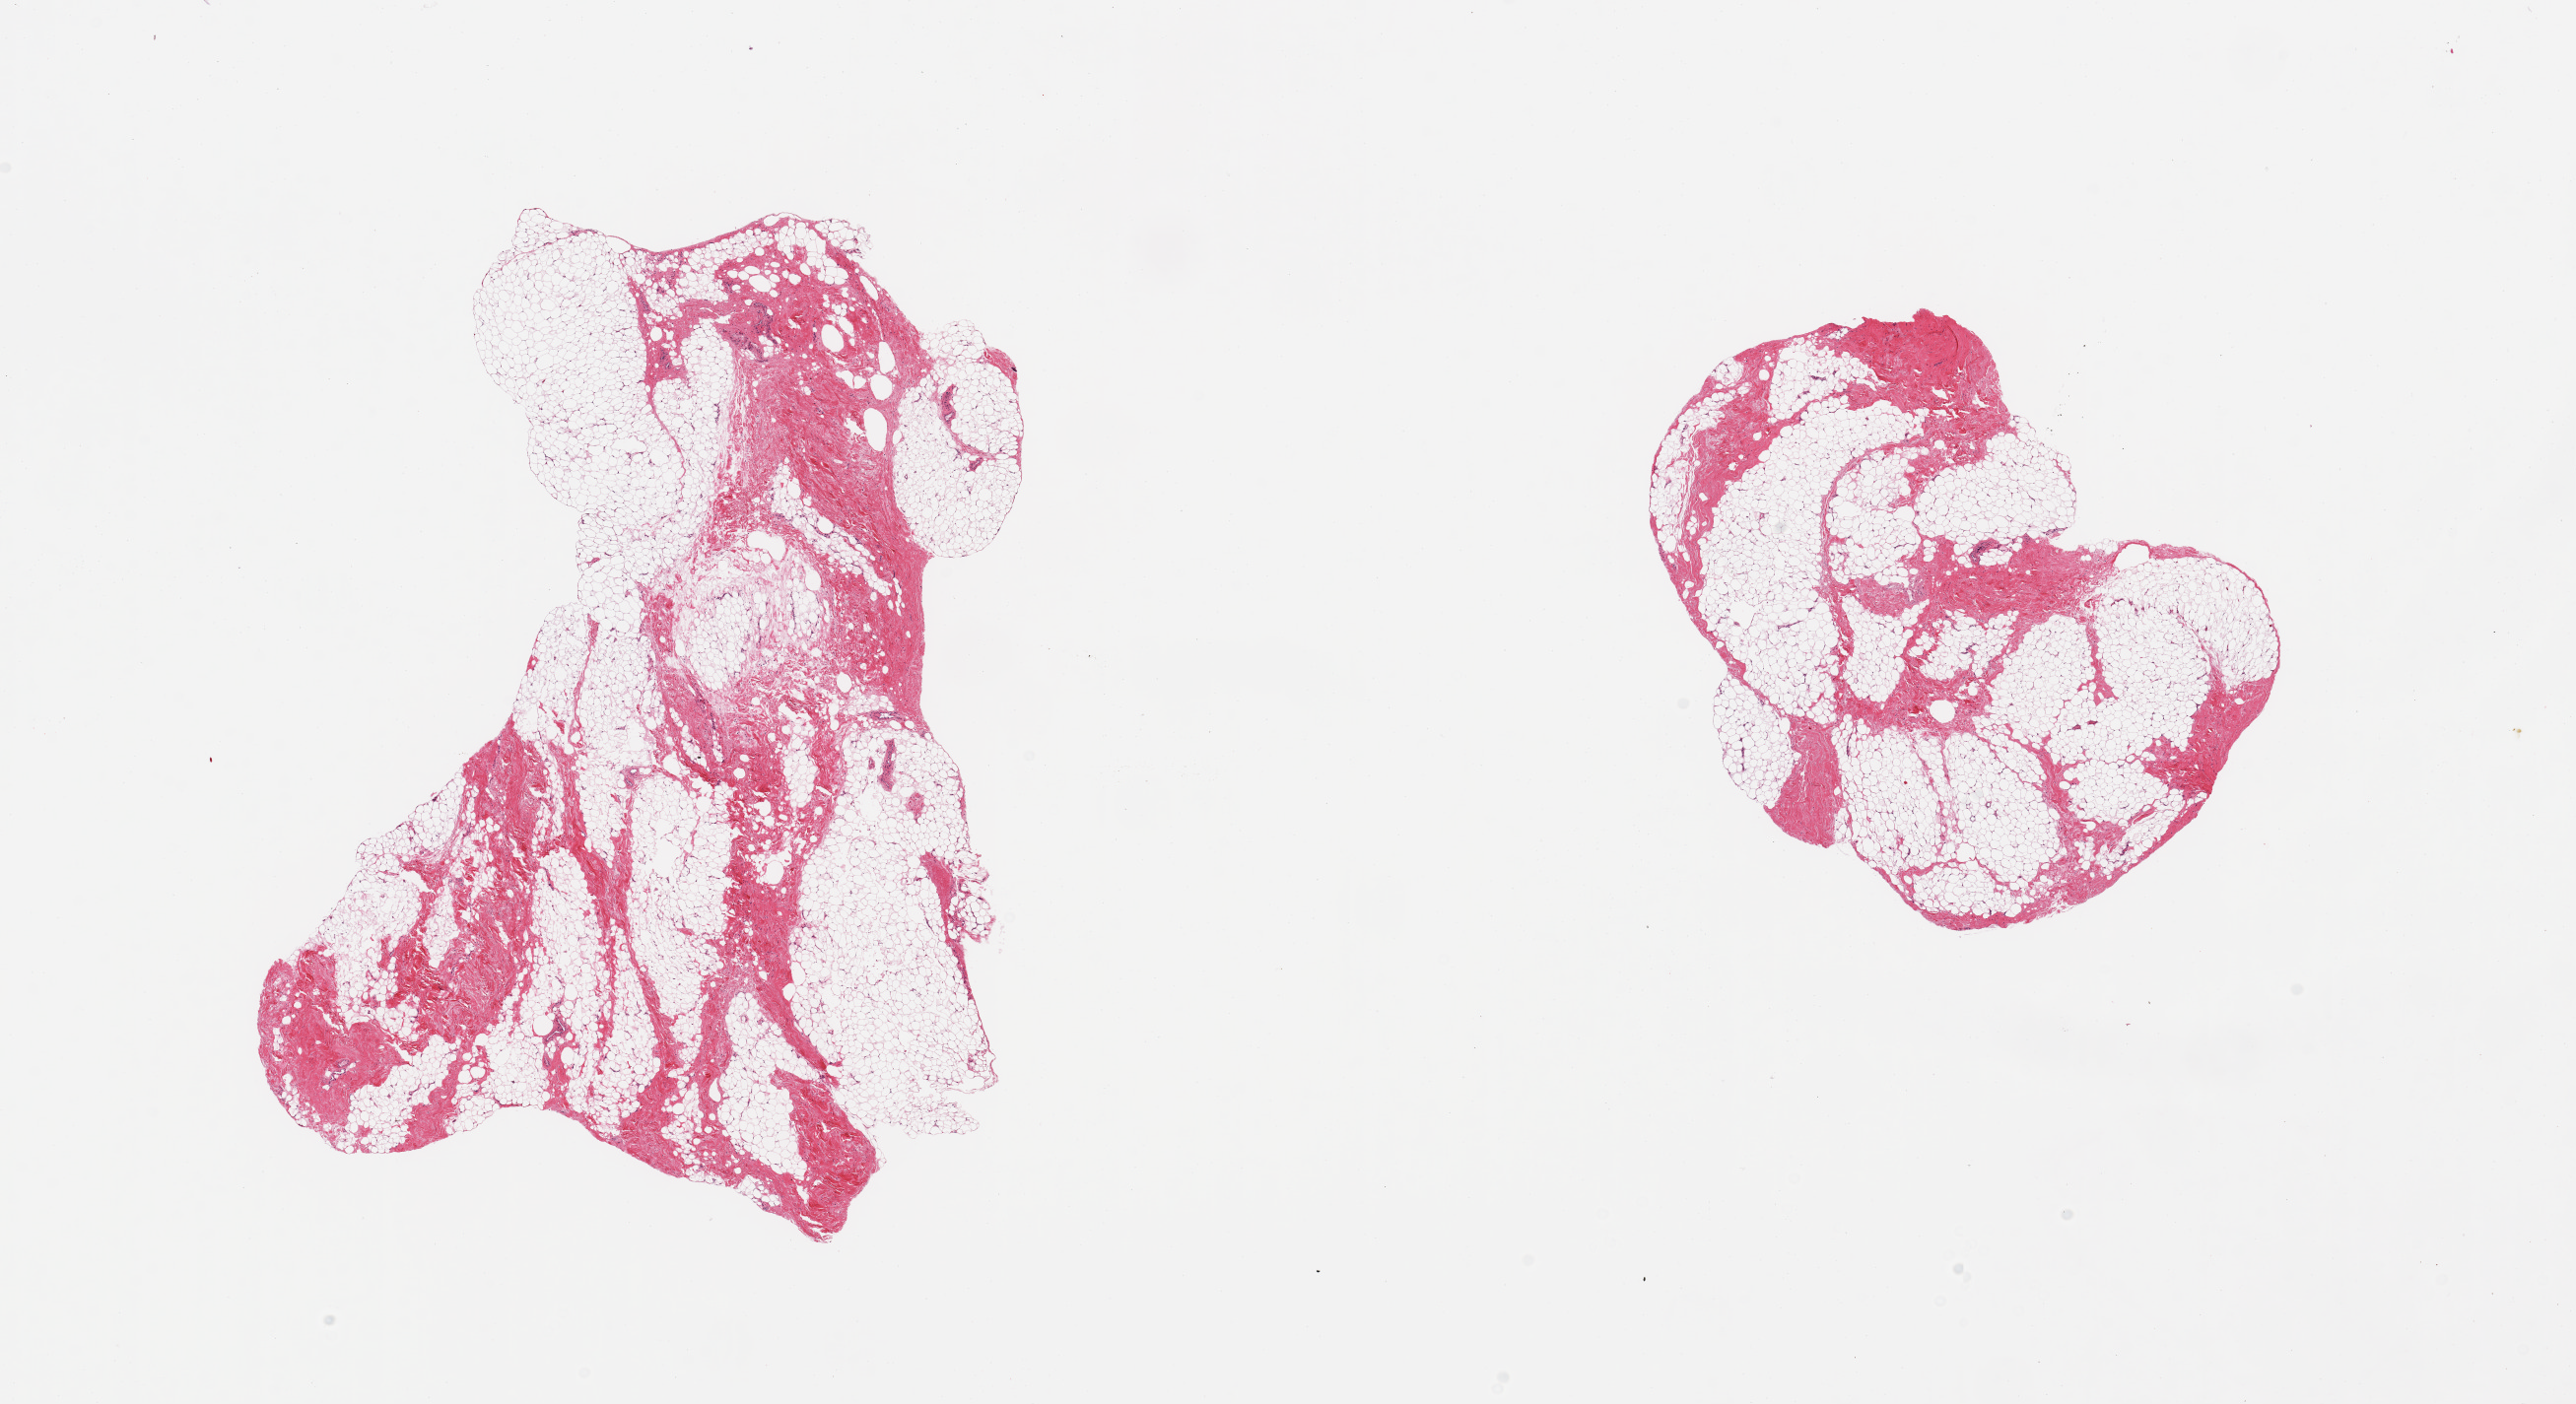
Whole-slide image, H&E stain — low-resolution overview of the scanned area, about 20.7 x 11.3 mm, PAXgene-fixed, paraffin-embedded tissue, sampled site (target tissue): breast, donor tissue sample. Male donor.
• pathologist's review note for this sample: 2 pieces, fibroadipose elements only